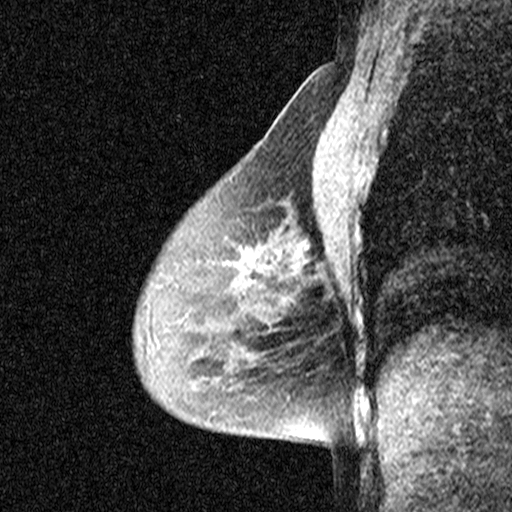
Breast MRI (dynamic contrast-enhanced), one sagittal slice; dynamic contrast-enhanced study with each time point stored as its own series, time point 2 of 3 at this slice position (early post-contrast, ordered by acquisition time); 1.5 T; TE 4.5 ms, TR 11 ms; 3 mm slice thickness; 512 × 512 image matrix, field of view 200 × 200 mm. Patient: female, 54 years. From the clinical record (not read from this slice): setting: breast cancer imaged before/during neoadjuvant chemotherapy; receptor status: HR-positive, HER2-negative.
Structures marked on this image (semi-automatic segmentation, software-assisted and operator-edited):
- analysis volume of interest (the breast-tissue region the enhancement analysis was run in; not a lesion): bounding box <214,200,333,325> (left, top, right, bottom; pixels)
- tumour enhancement mask (voxels above the 90 % enhancement threshold inside the analysis volume of interest): <251,263,254,265>